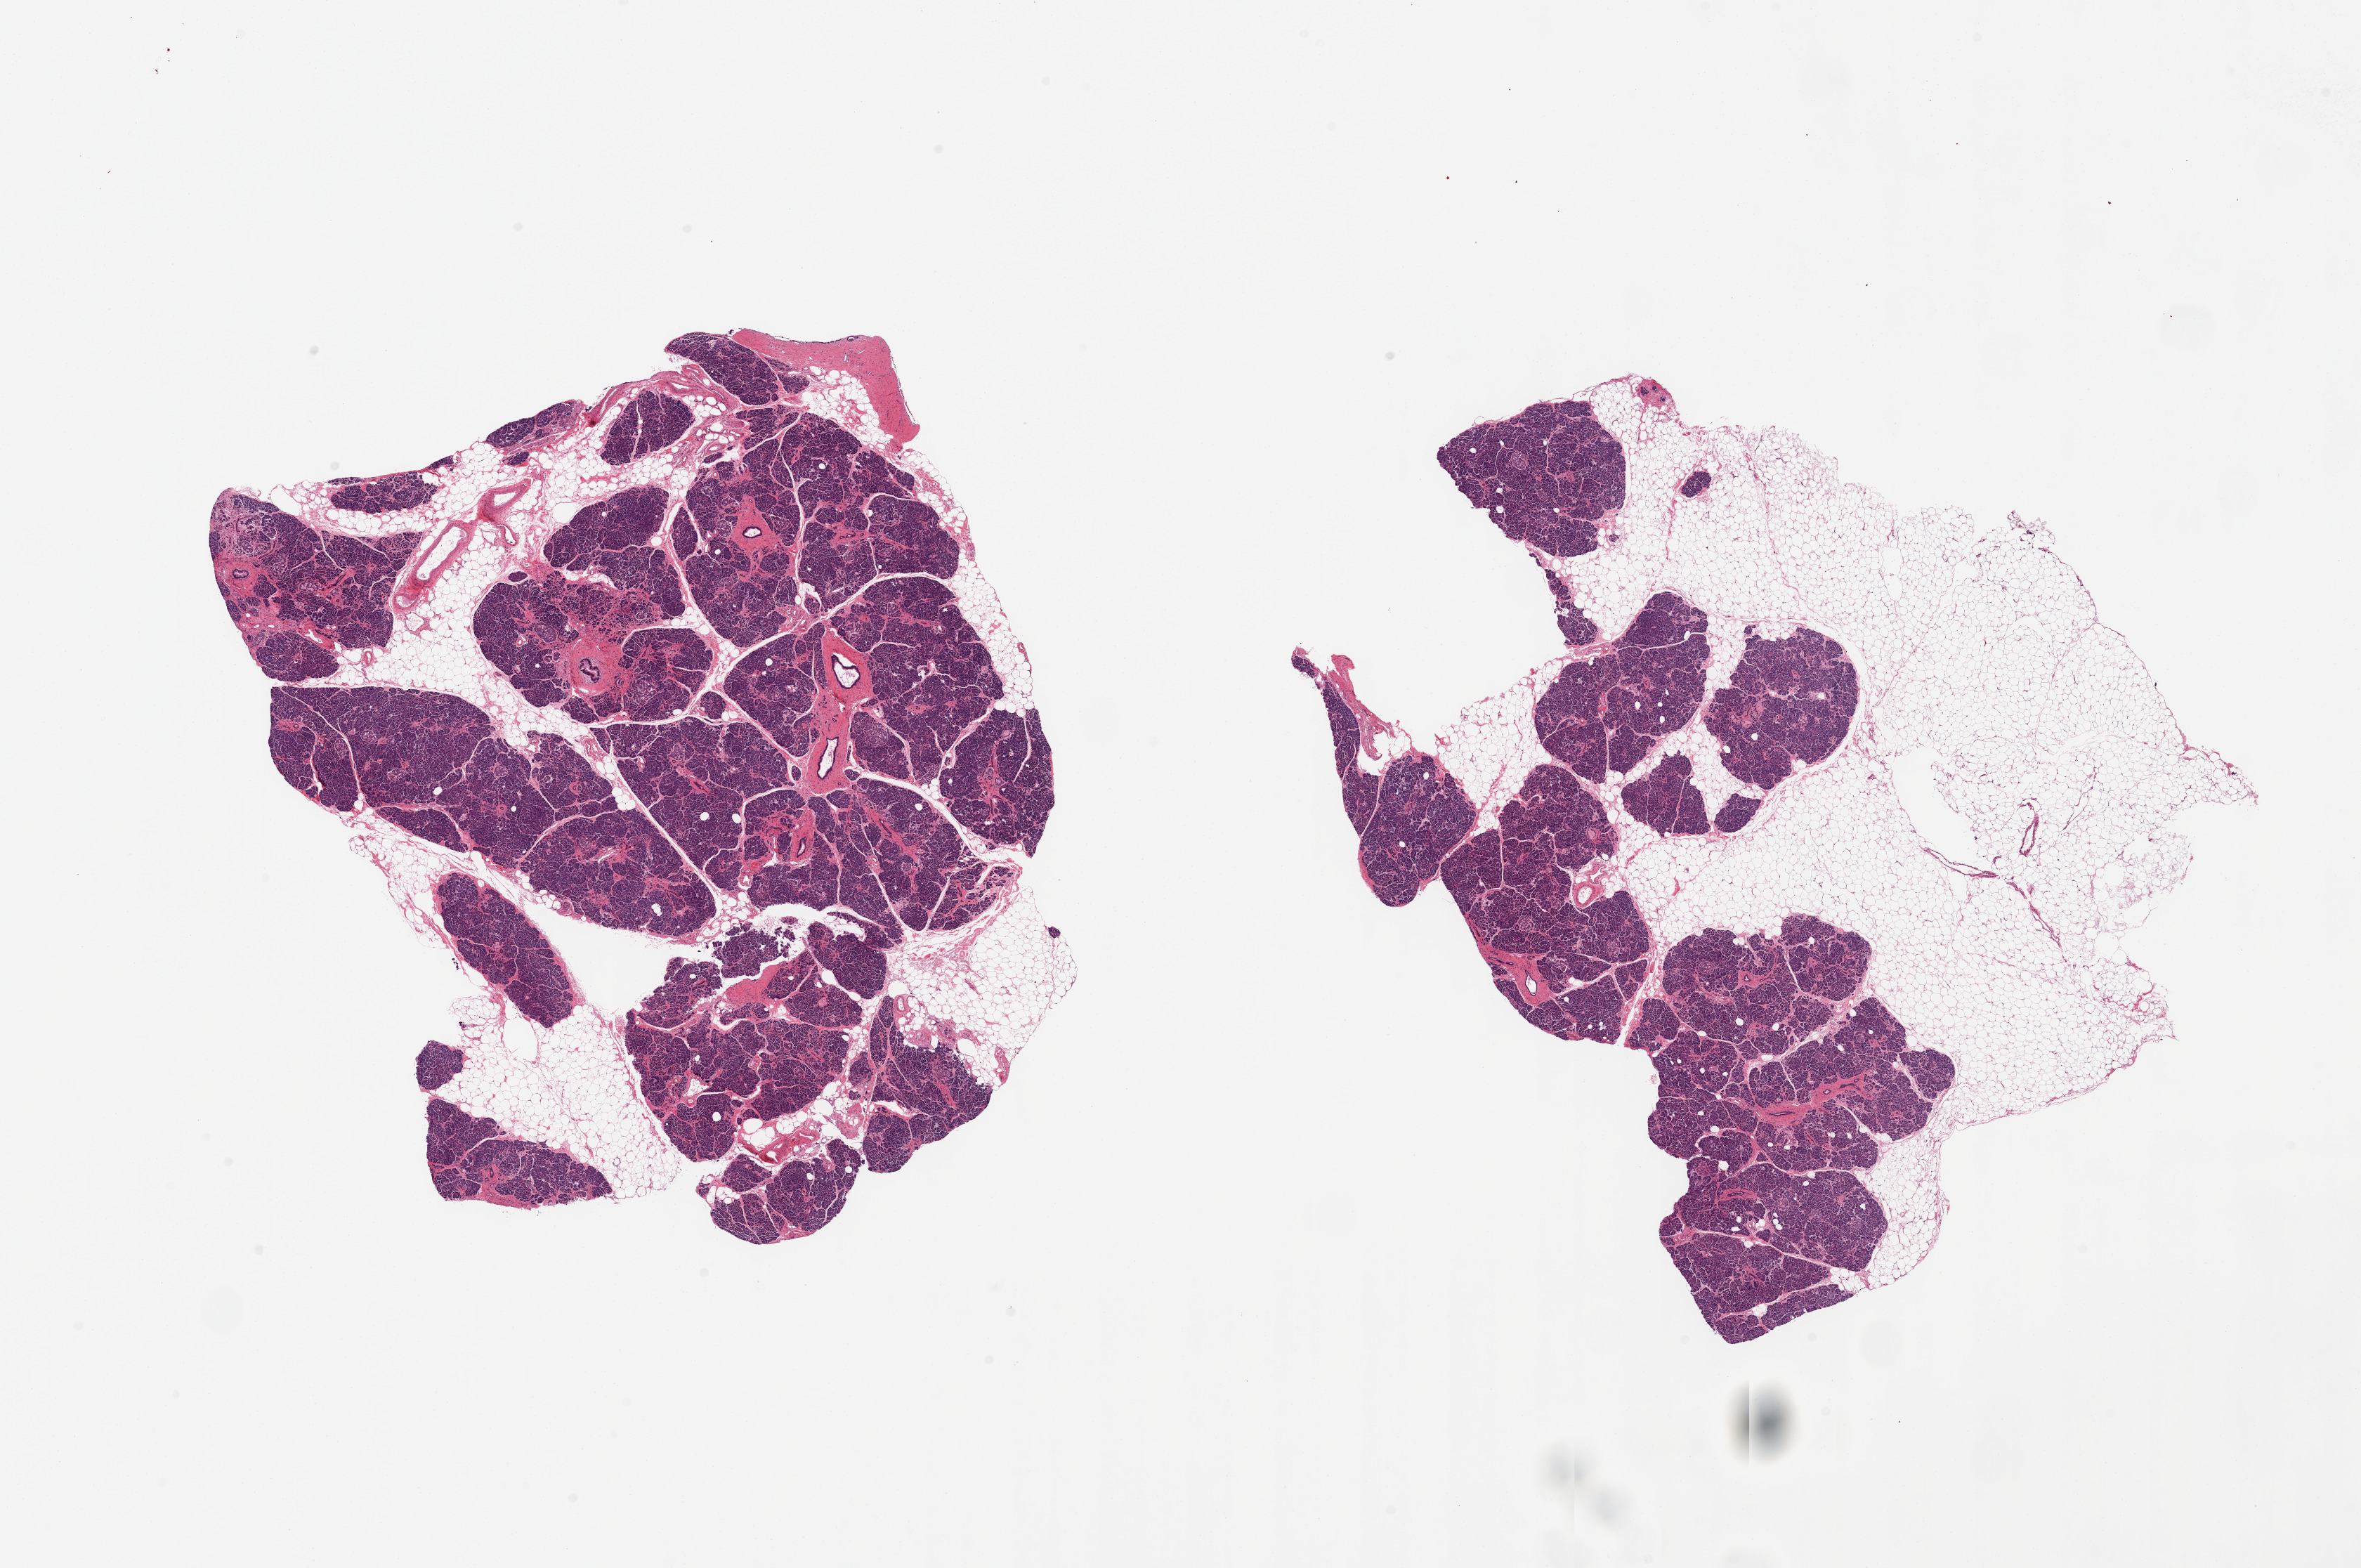
Digitized hematoxylin and eosin (H&E)-stained section, whole scanned area (about 26.6 x 17.7 mm) shown as a low-resolution overview. PAXgene-fixed paraffin-embedded (PFPE) section. Target tissue: pancreas. Donor tissue sample. Donor: male.
Reviewer comment on this tissue sample: 2 pieces; 20 & 60% internal & external fat content.